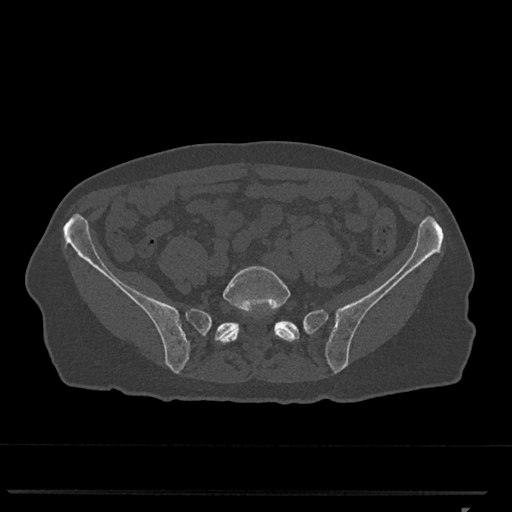
CT including the spine, one axial slice; slice 130 of 793 in the series (ordered by position); bone window (W 1800 / L 400 HU); 0.5 mm slice thickness; 512 × 512 image matrix, field of view 380 × 380 mm. Female patient, age 62 years. Case-level facts recorded for this patient, not image findings: primary cancer: renal.
Structures marked on this image (semi-automatically segmented with operator editing):
- L5 vertebra: bounding box (x1, y1, x2, y2) in pixels: (218, 266, 297, 344)